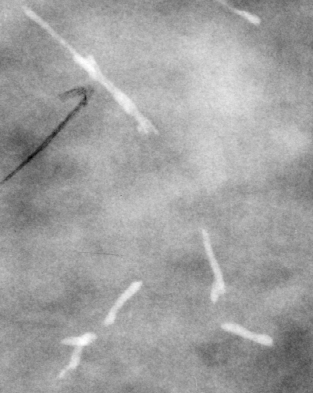
Cropped region of a digitized screen-film mammogram centred on a radiologist-marked abnormality; left breast; CC view.
Finding: calcifications, morphology large rodlike / round and regular, distribution regional; BI-RADS assessment category 2; subtlety rating 5 on a 1 (subtle) to 5 (obvious) scale; benign; no additional work-up was recommended (benign without callback).